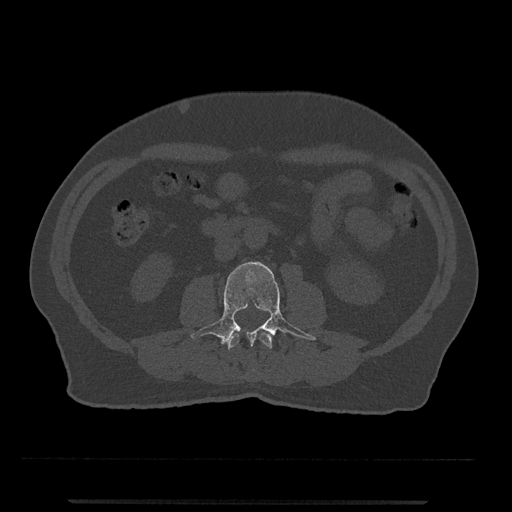
CT including the spine, one axial slice. Position 210 of 797 along the scan axis. Reconstruction kernel Br40s/3. Bone window (W 1800 / L 400 HU). 0.5 mm slice thickness. 512 × 512 image matrix. Male patient, age 63 years. From the clinical record (not read from this slice): primary cancer: prostate.
Structures marked on this image (semi-automatically segmented with operator editing):
- L2 vertebra: bounding box <227,332,272,378> (left, top, right, bottom; pixels)
- L3 vertebra: <191,262,316,346>